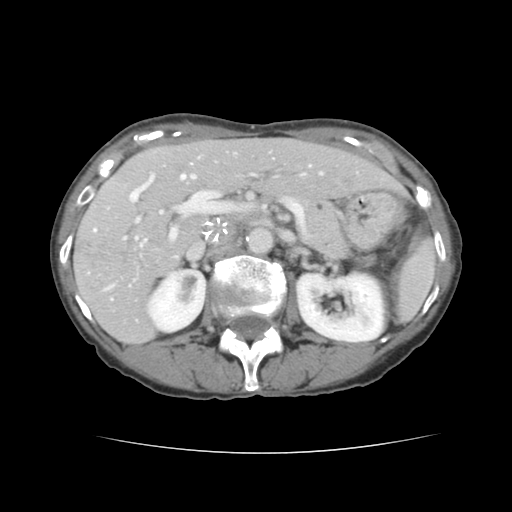
Contrast-enhanced abdominal CT, one axial slice. Slice 78 of 136 in the series (ordered by position). 120 kVp. Intravenous contrast given. Soft-tissue window (W 400 / L 40 HU). 2.5 mm slice thickness. 512 × 512 image matrix. Female patient, age 77 years. Case-level facts recorded for this patient, not image findings: diagnosis: colorectal cancer liver metastases, imaged before liver resection; multiple liver metastases: yes; largest metastasis: 3 cm; chemotherapy before resection: yes.
Annotated regions visible in this slice (expert manual segmentation):
- hepatic veins: bounding box [x1, y1, x2, y2] px = [135, 173, 322, 239]
- liver: [75, 139, 401, 343]
- planned liver remnant (the part of the liver to remain after resection): [155, 139, 401, 199]
- portal vein (with intrahepatic branches): [94, 174, 305, 289]
- liver metastasis: [167, 221, 175, 232]